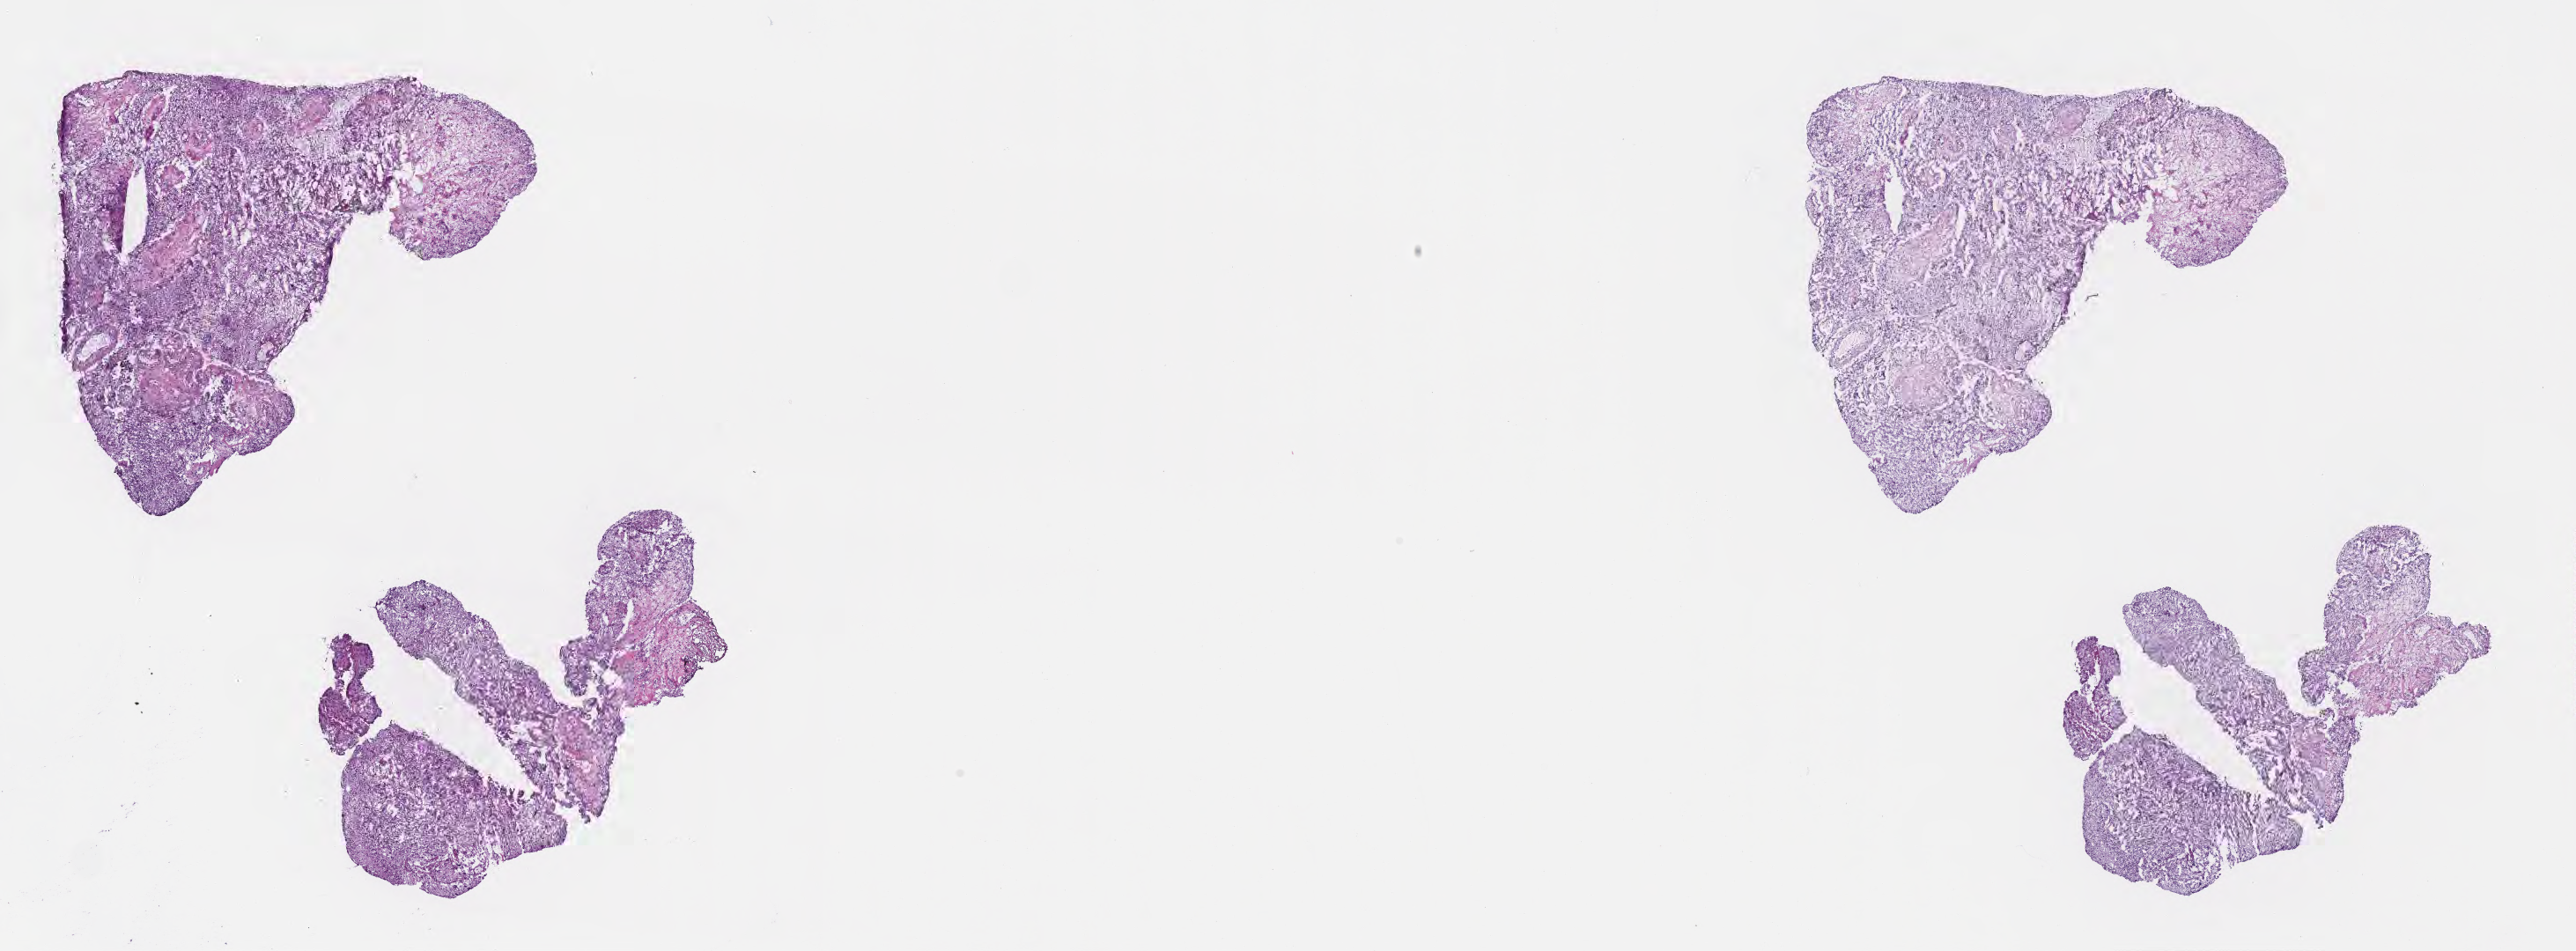
Whole-slide image, hematoxylin and eosin (H&E) stain, shown as a low-resolution overview of the whole scanned area (about 23.6 x 8.7 mm). Cryosection. Recurrent tumor. Anatomic site: brain. Male, age 41 years at initial diagnosis. Composition of this section per pathologist review: tumor cells 57%, tumor nuclei 73%, stromal cells 20%, necrosis 2%, normal cells 21%. Inflammatory infiltration, as recorded: lymphocyte infiltration 0%, monocyte infiltration 0%, neutrophil infiltration 0%.
• patient diagnosis: Glioblastoma, NOS